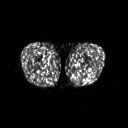
FDG PET of an extremity soft-tissue mass (from a PET/CT study), one axial slice; 128 × 128 image matrix. Patient: male, 27 years. From the clinical record (not read from this slice): histological type: extraskeletal osteosarcoma; grade: high; site of the primary tumour: left adductur.
Annotated regions visible in this slice (expert contour drawn on MRI and transferred to this co-registered scan by the dataset authors):
- gross tumour volume (mass): bounding box <77,63,88,68> (left, top, right, bottom; pixels)